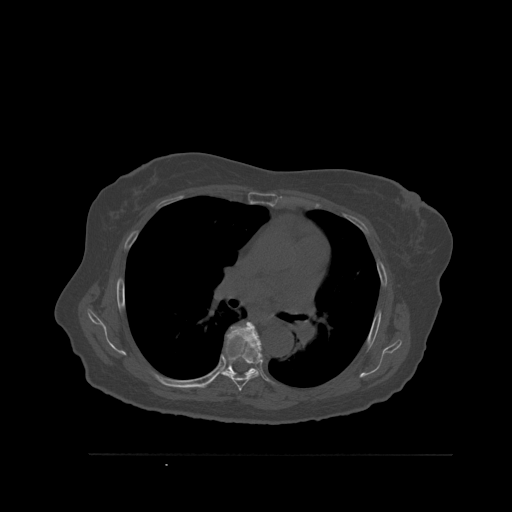
CT including the spine, one axial slice. Slice 375 of 527 in the series (ordered by position). Bone window (W 1800 / L 400 HU). 1.5 mm slice thickness. 512 × 512 image matrix, field of view 470 × 470 mm. Female patient, age 73 years. From the clinical record (not read from this slice): primary cancer: breast; vertebrae with lytic lesions (as recorded): L2.
Structures marked on this image (semi-automatic segmentation, software-assisted and operator-edited):
- T6 vertebra: bounding box <222,322,263,391> (left, top, right, bottom; pixels)
- T7 vertebra: <224,350,257,377>